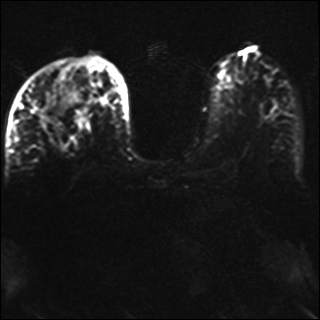
Breast MRI, one axial slice; slice 16 of 42 in the series (ordered by position); diffusion-weighted series; image 2 of 4 stored at this slice position (different b-values; order by instance number); 1.5 T; 4 mm slice thickness; 320 × 320 image matrix, field of view 330 × 330 mm. Female patient.
Outlined on this slice (outlined manually by an expert reader):
- tumour on diffusion-weighted imaging: bounding box <40,114,47,127> (left, top, right, bottom; pixels)